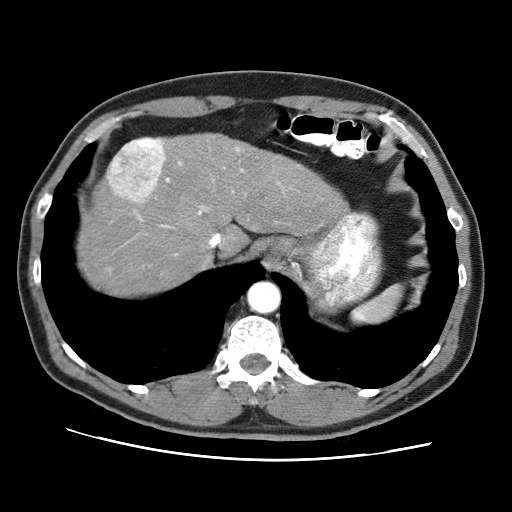
Contrast-enhanced abdominal CT (liver protocol), one axial slice; slice 57 of 71 in the series (ordered by position); reconstruction kernel STANDARD; 120 kVp; soft-tissue window (W 400 / L 40 HU); 2.5 mm slice thickness; 512 × 512 image matrix, field of view 360 × 360 mm. Case-level facts recorded for this patient, not image findings: diagnosis: hepatocellular carcinoma (patient treated with transarterial chemoembolisation; whether this scan precedes or follows treatment is not stated here); TNM stage (as recorded): Stage-II; Child-Pugh class: A; tumour differentiation: well differentiated; tumour nodularity: multinodular.
Outlined on this slice (semi-automatic segmentation, software-assisted and operator-edited):
- liver parenchyma outside the tumour (the mass and vessels are separate outlines, so this box may not span the whole liver): box from (x=80, y=134) to (x=346, y=294) px
- mass: (x=107, y=139)–(x=165, y=204)
- liver vessels: (x=158, y=140)–(x=239, y=227)